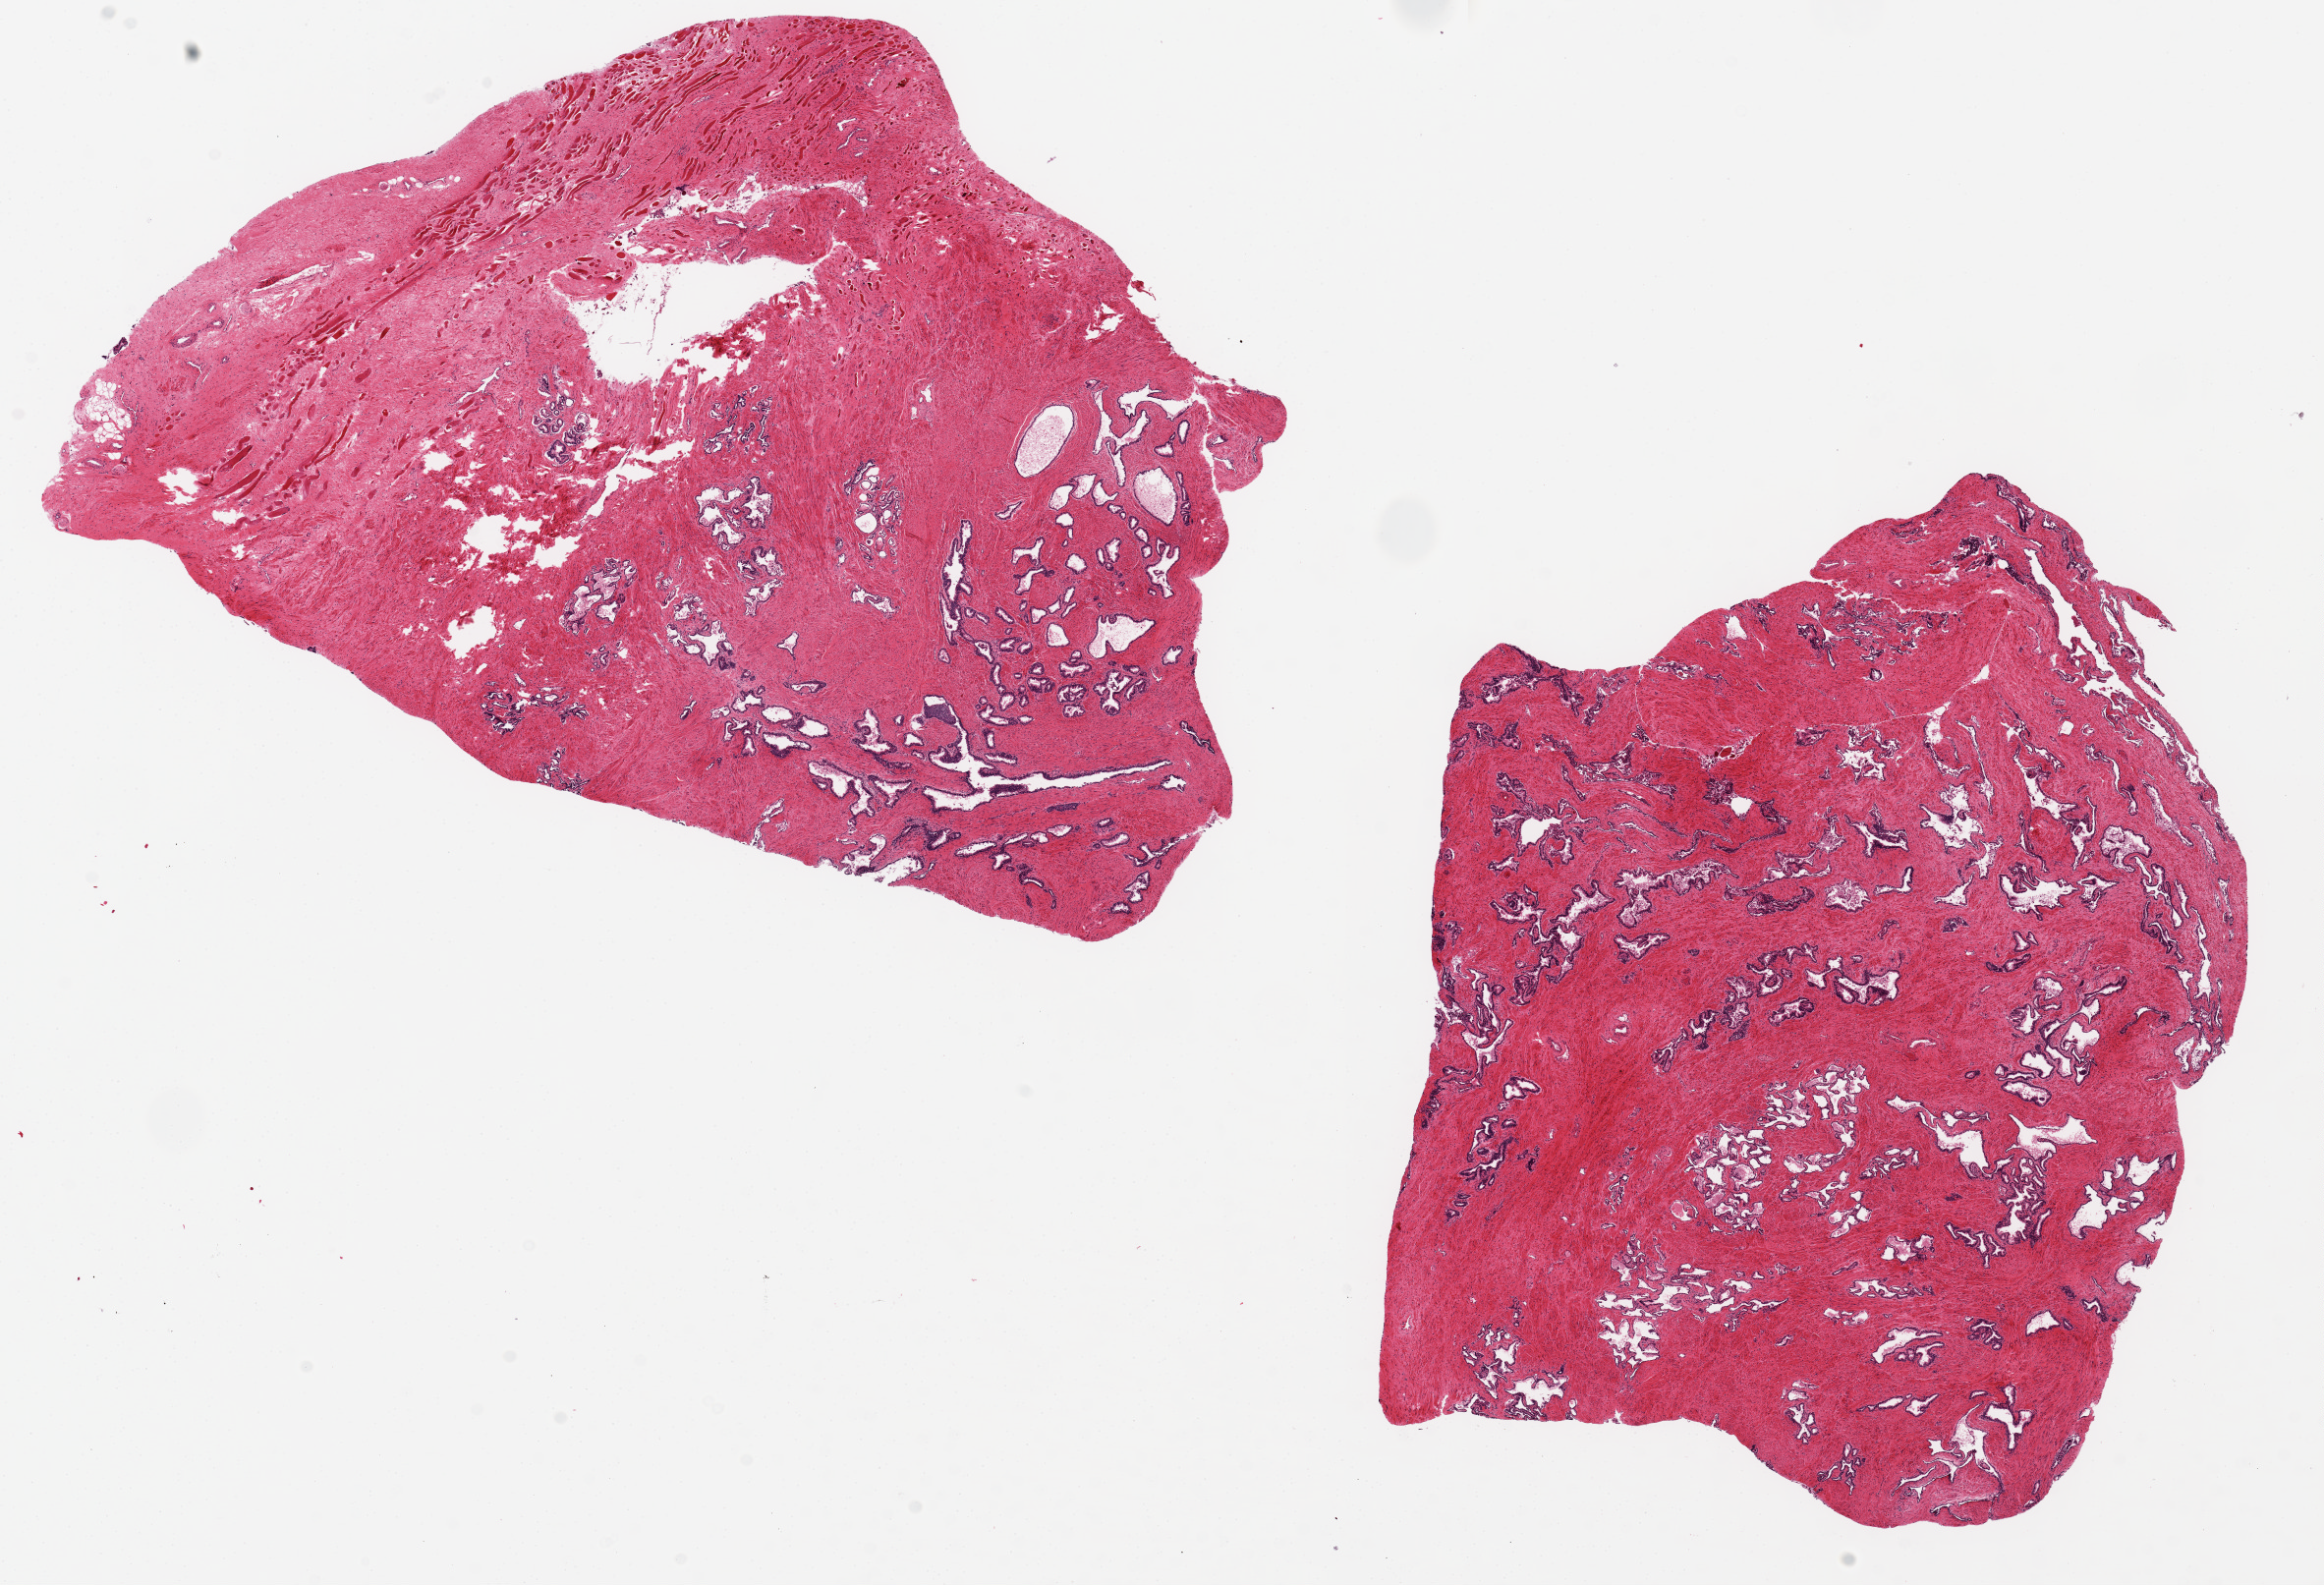
Digitized haematoxylin and eosin-stained section — low-resolution overview of the scanned area, about 18.7 x 12.8 mm; PAXgene-fixed, paraffin-embedded tissue; sampled site (target tissue): prostate; tissue donor sample.
Pathologist's review note for this sample: 2 ~9x6.5mm aliquots, patchy glandular hyperplasia and atrophy.